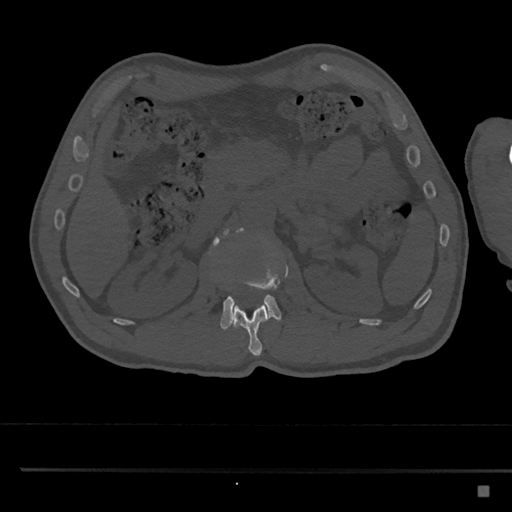
CT including the spine, one axial slice; position 797 of 797 along the scan axis; bone window (W 1800 / L 400 HU); 512 × 512 image matrix, field of view 391 × 391 mm. Patient: male, 59 years. From the clinical record (not read from this slice): primary cancer: prostate.
Annotated regions visible in this slice (semi-automatically segmented with operator editing):
- L1 vertebra: bounding box [x1, y1, x2, y2] px = [233, 303, 269, 356]
- L2 vertebra: [209, 230, 282, 329]